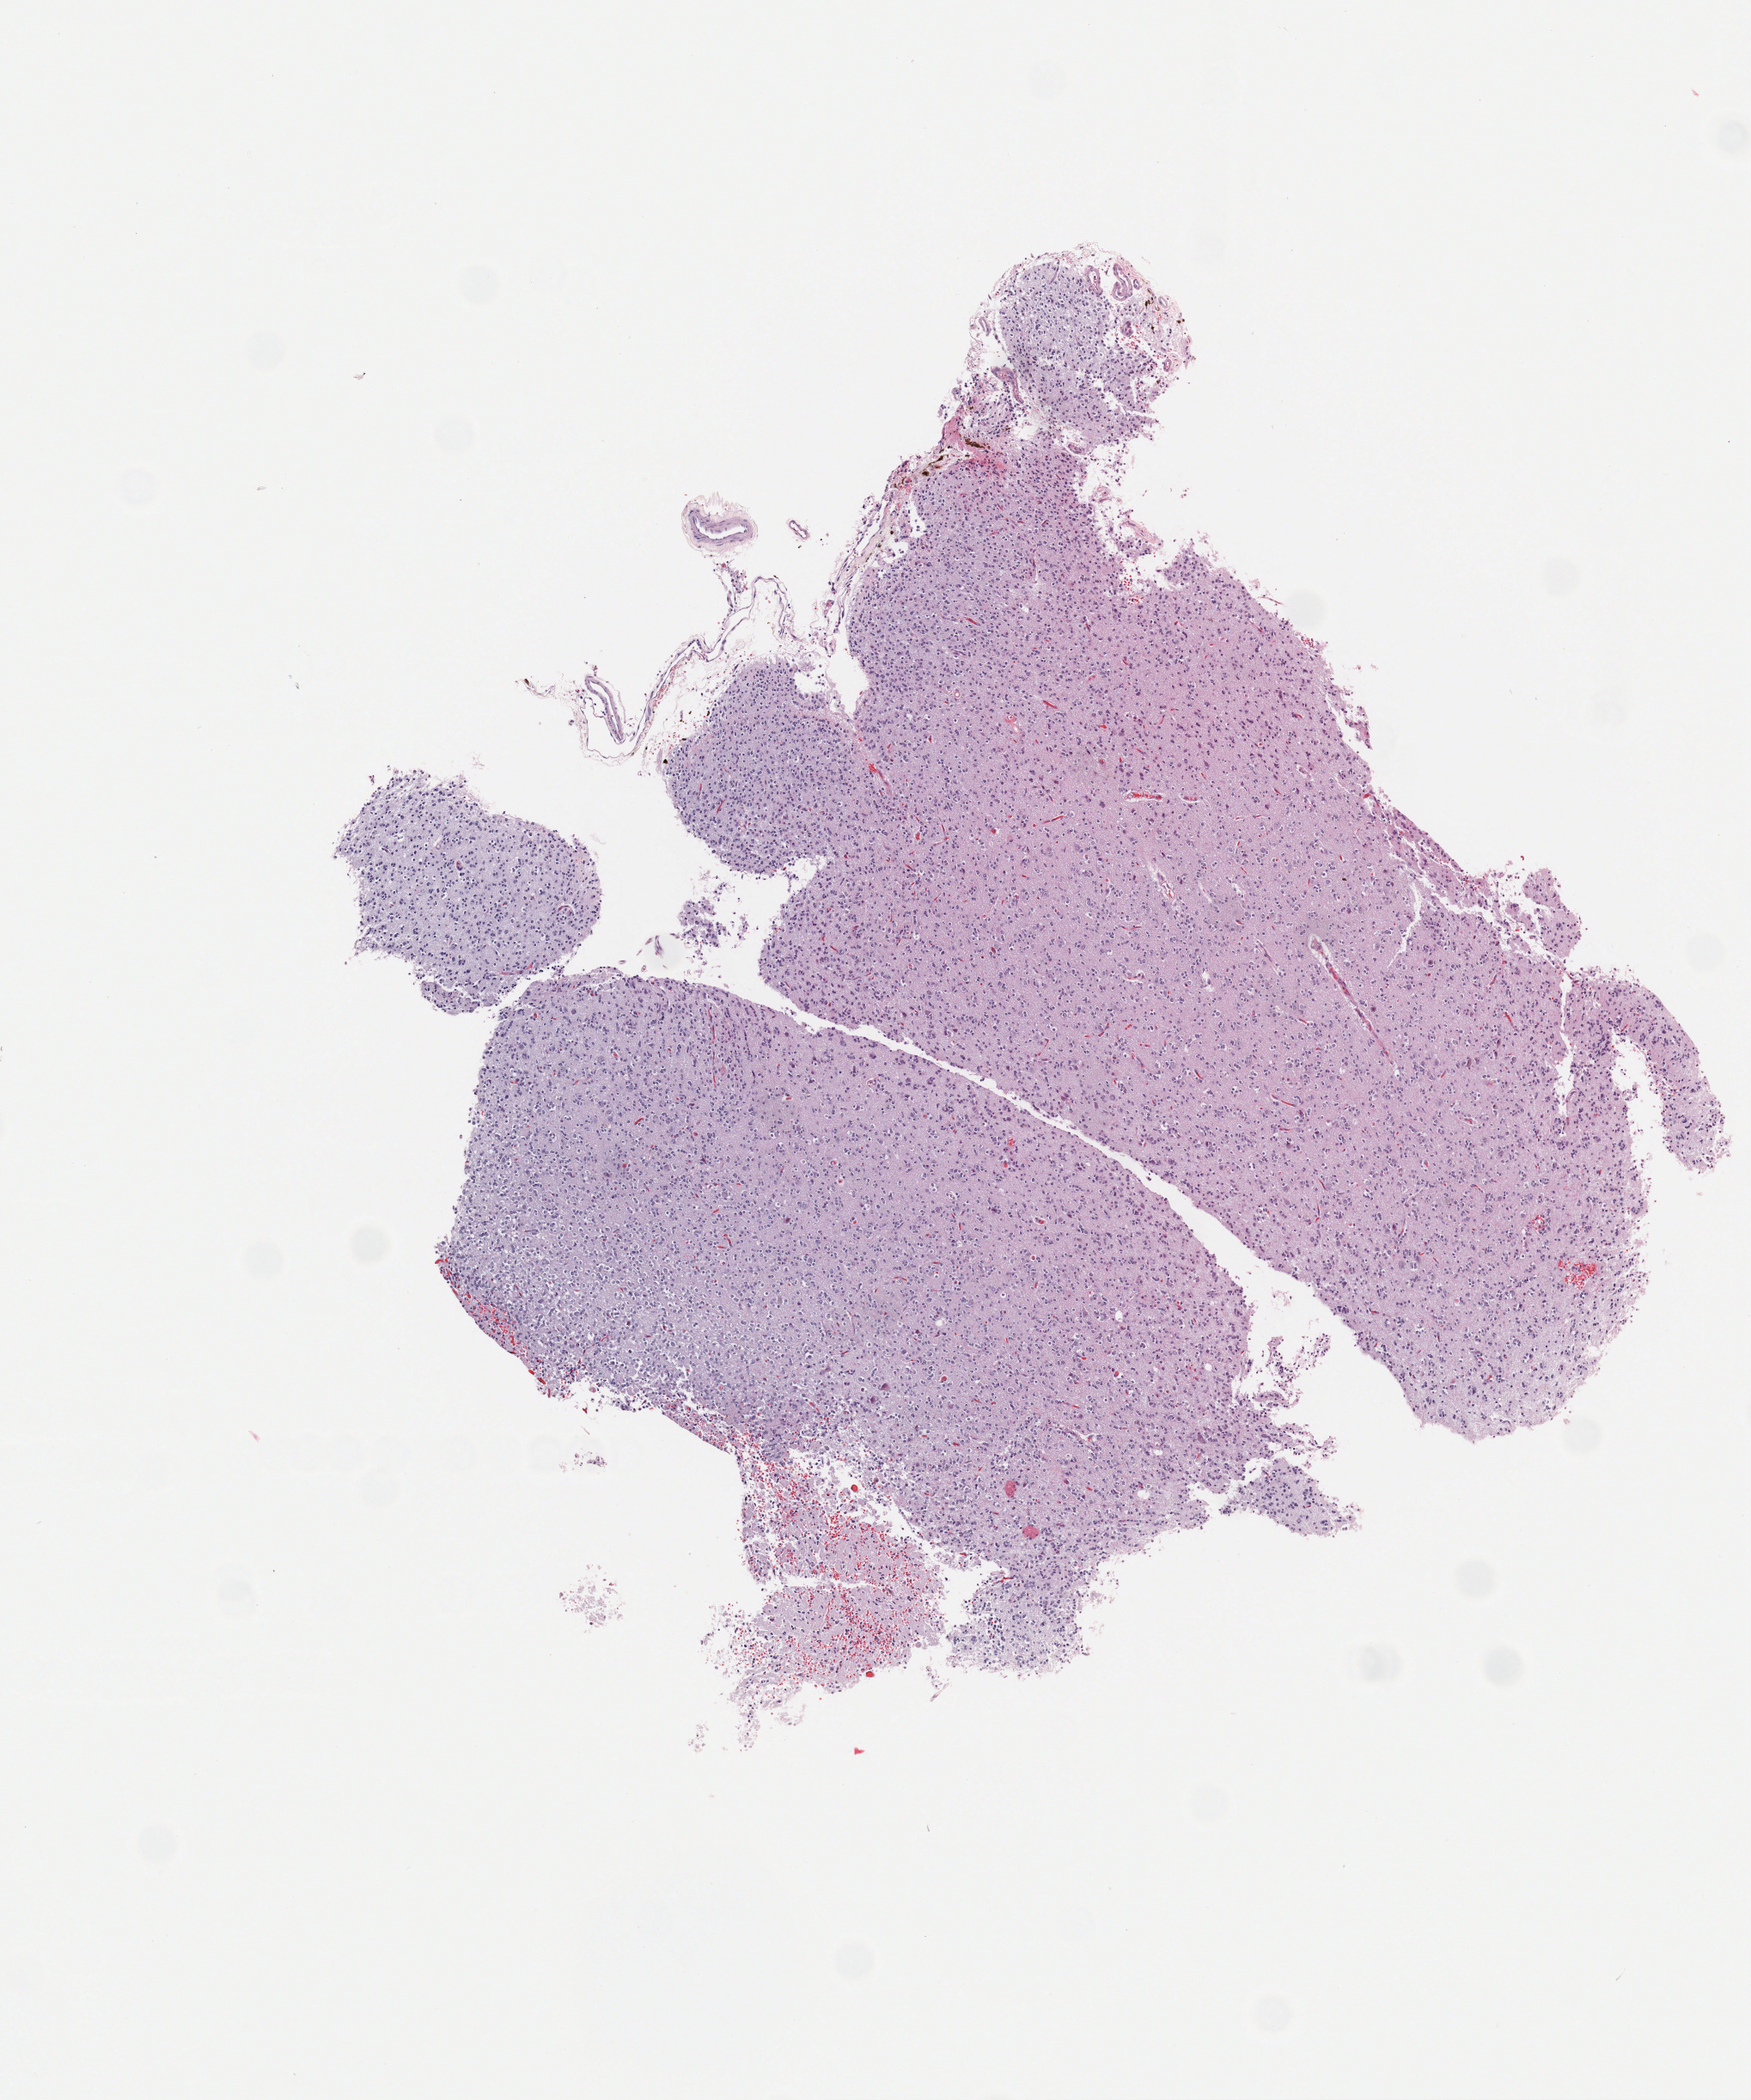
H&E whole-slide image — shown as a low-resolution overview of the whole scanned area (about 4.1 x 4.9 mm, slide scanned at 40x), FFPE section, primary tumour sample from the brain. Male, age 51 years at initial diagnosis. Histologic grade: G2 (moderately differentiated).
Pathologic diagnosis: Oligodendroglioma, NOS (cerebrum).